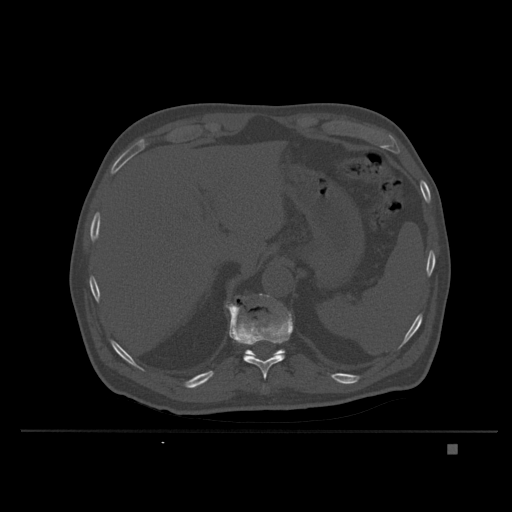
CT including the spine, one axial slice. Position 173 of 435 along the scan axis. Bone window (W 1800 / L 400 HU). 512 × 512 image matrix. Patient: male, 73 years. From the clinical record (not read from this slice): primary cancer: skin.
Outlined on this slice (semi-automatically segmented with operator editing):
- T10 vertebra: box from (x=263, y=386) to (x=267, y=389) px
- T11 vertebra: (x=228, y=304)–(x=294, y=380)
- T12 vertebra: (x=227, y=305)–(x=285, y=359)